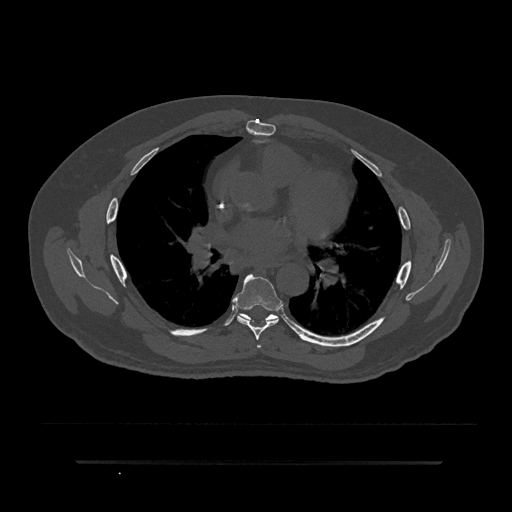
CT including the spine, one axial slice; position 512 of 797 along the scan axis; reconstruction kernel Br40s/3; 120 kVp; bone window (W 1800 / L 400 HU); 0.5 mm slice thickness; 512 × 512 image matrix, field of view 464 × 464 mm. Male patient, age 59 years. Case-level facts recorded for this patient, not image findings: primary cancer: bile ducts.
Annotated regions visible in this slice (semi-automatic segmentation, software-assisted and operator-edited):
- T5 vertebra: bounding box (x1, y1, x2, y2) in pixels: (257, 345, 261, 348)
- T6 vertebra: (233, 273, 282, 341)
- T7 vertebra: (241, 314, 276, 322)